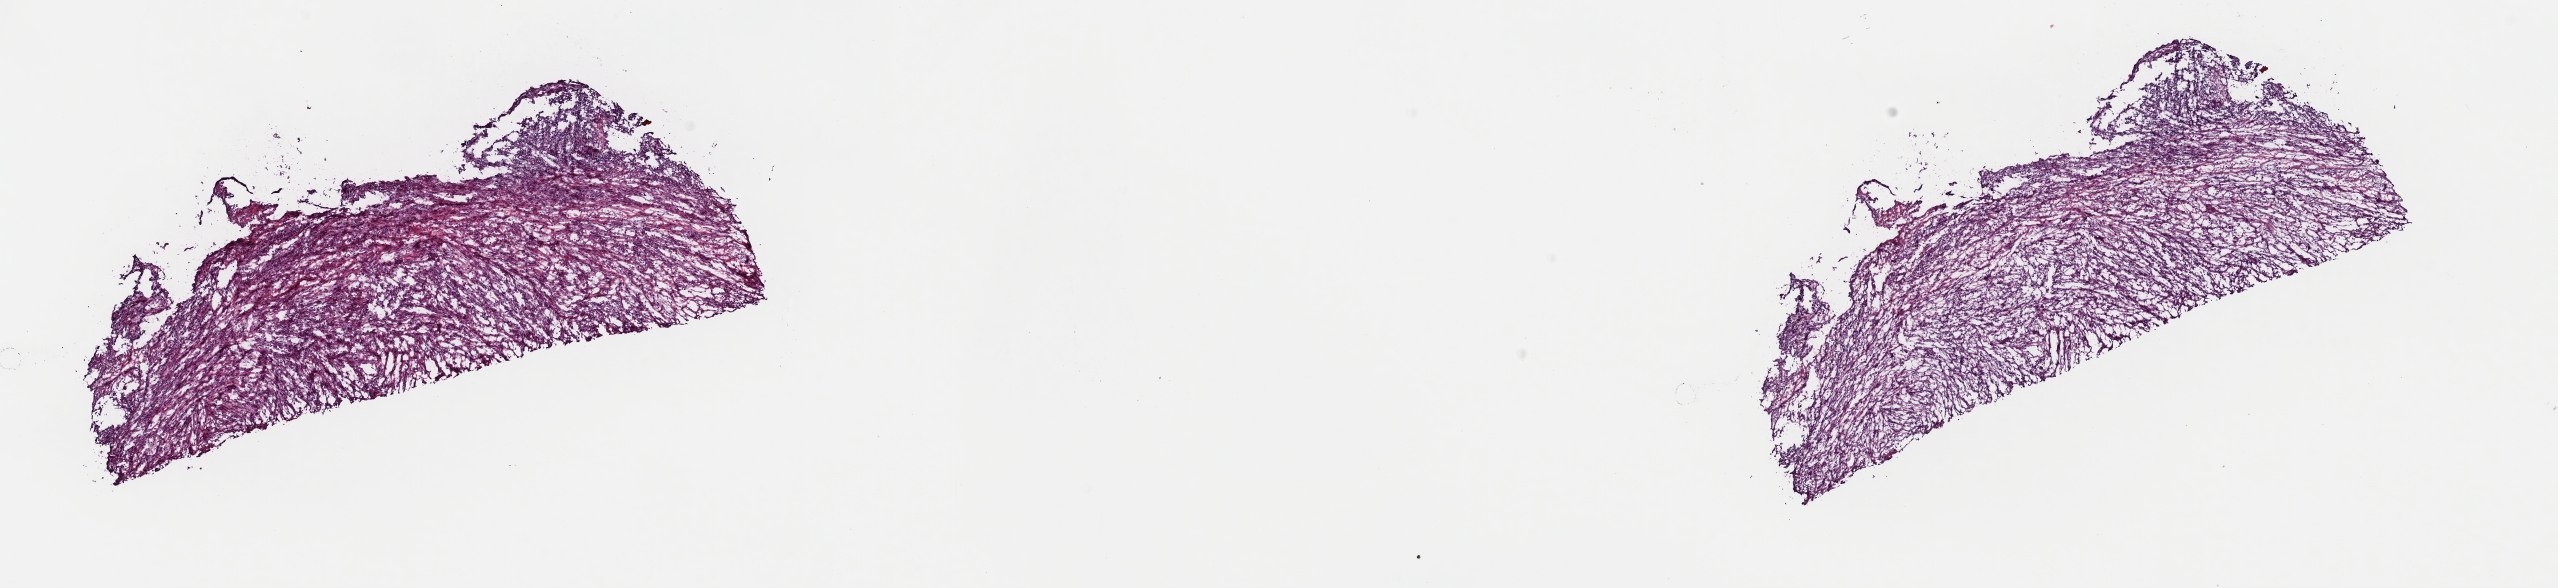
H&E-stained whole-slide image, low-resolution overview of the scanned area, about 20.2 x 4.6 mm, frozen section from the top of the tissue portion, primary tumour sample from the bones, joints and articular cartilage of limbs. Female patient; age at initial diagnosis 47 years. Composition of this section per pathologist review: tumour cells 100%, tumour nuclei 92%, normal cells 0%, stromal cells 0%, necrosis 0%. Inflammatory infiltration, as recorded: lymphocyte infiltration 0%, monocyte infiltration 0%, neutrophil infiltration 0%.
Diagnosis: Leiomyosarcoma, NOS (short bones of lower limb and associated joints).